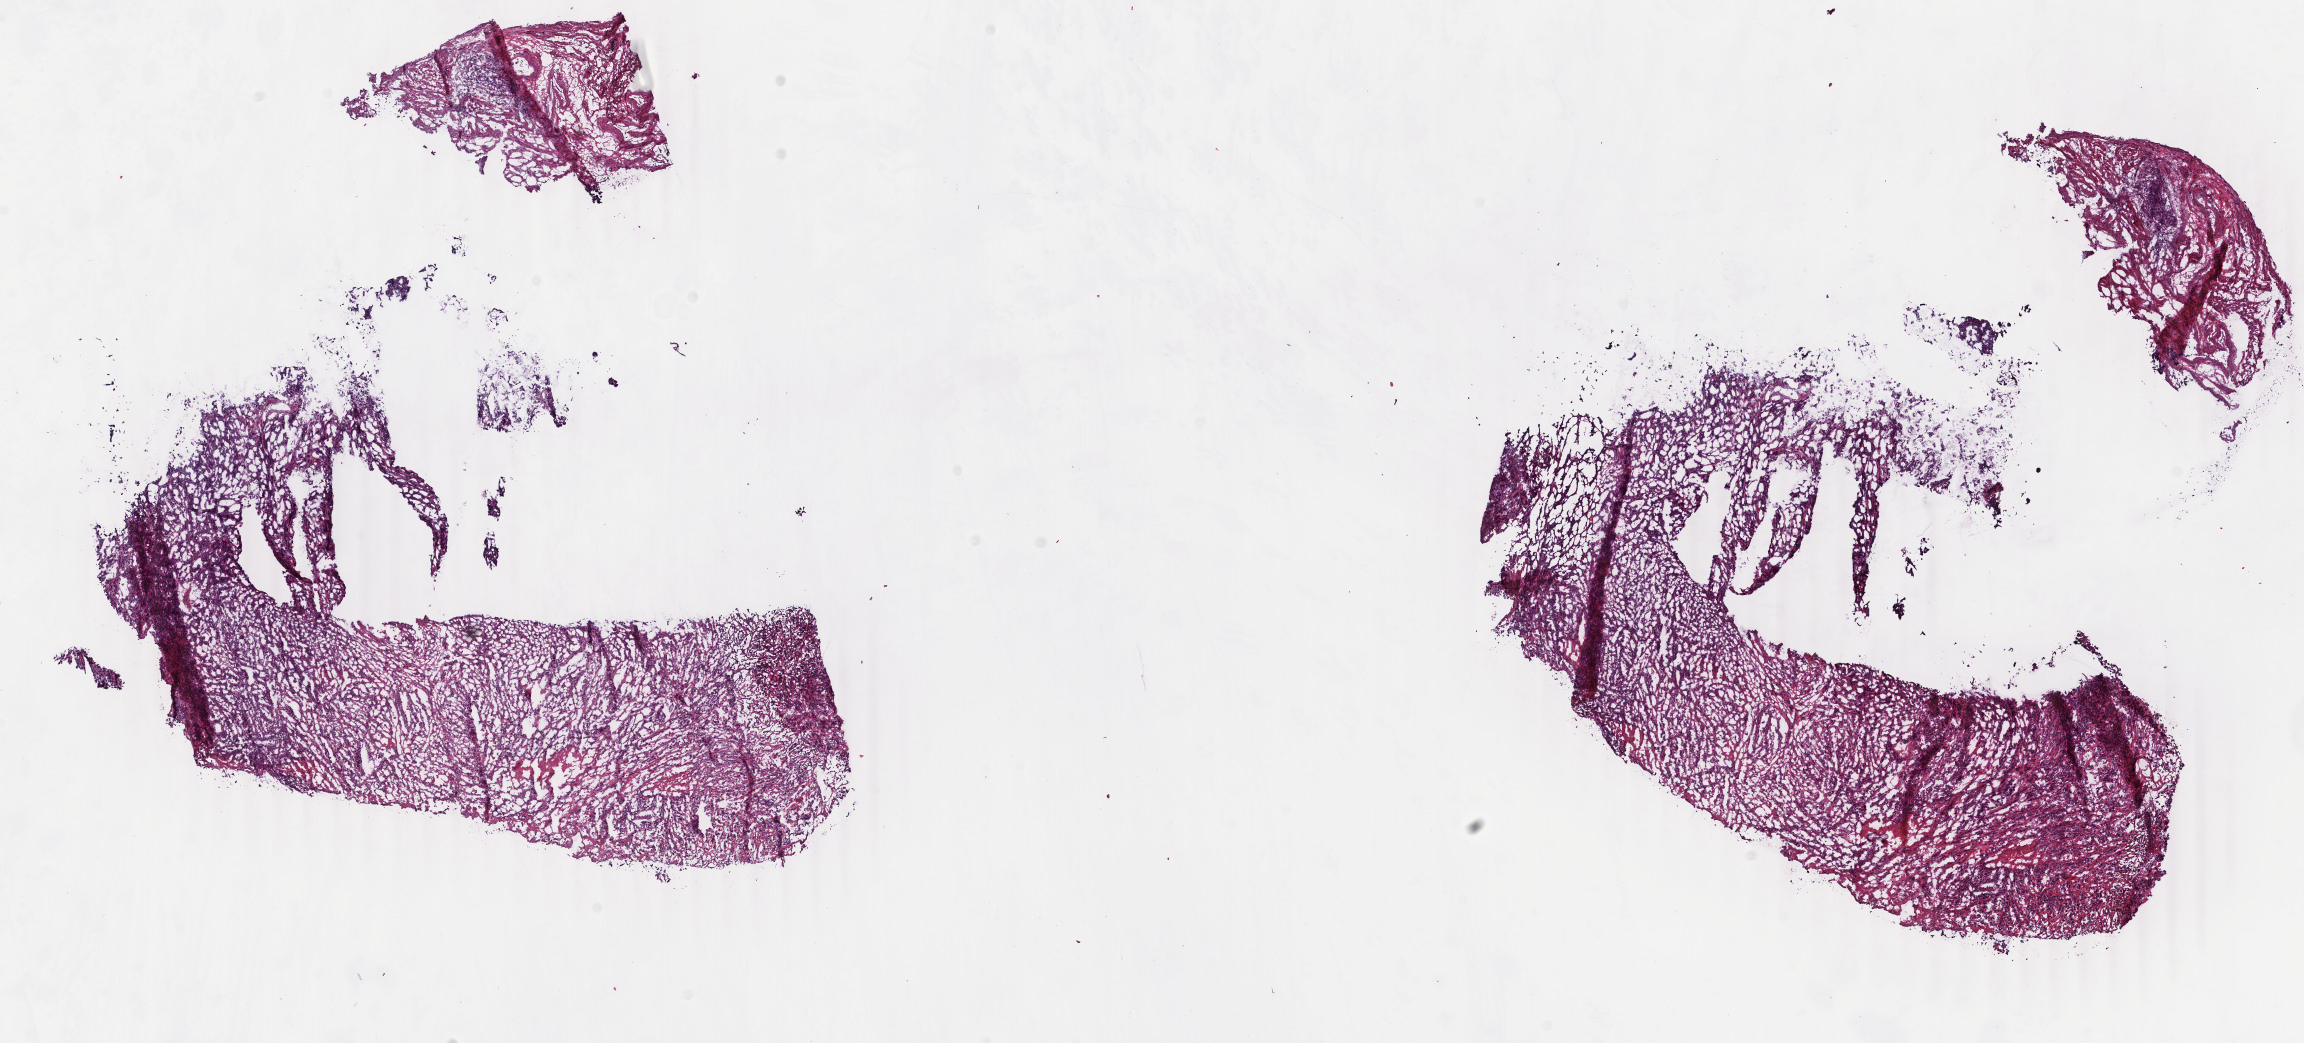
Whole-slide histology image, H&E-stained — low-resolution overview of the scanned area, about 18.3 x 8.3 mm (from a 40x scan); frozen section from the top of the tissue portion; sample: primary tumour, uterus. Female, age 75 years at initial diagnosis. Histologic grade: G3 (poorly differentiated). Pathologist review of this section (percent, as recorded): tumour cells 65%, tumour nuclei 75%, normal cells 15%, stromal cells 10%, necrosis 10%. Inflammatory infiltration, as recorded: lymphocyte infiltration 3%, monocyte infiltration 0%, neutrophil infiltration 0%.
- FIGO stage: IB
- pathologic diagnosis: Serous cystadenocarcinoma, NOS (endometrium)